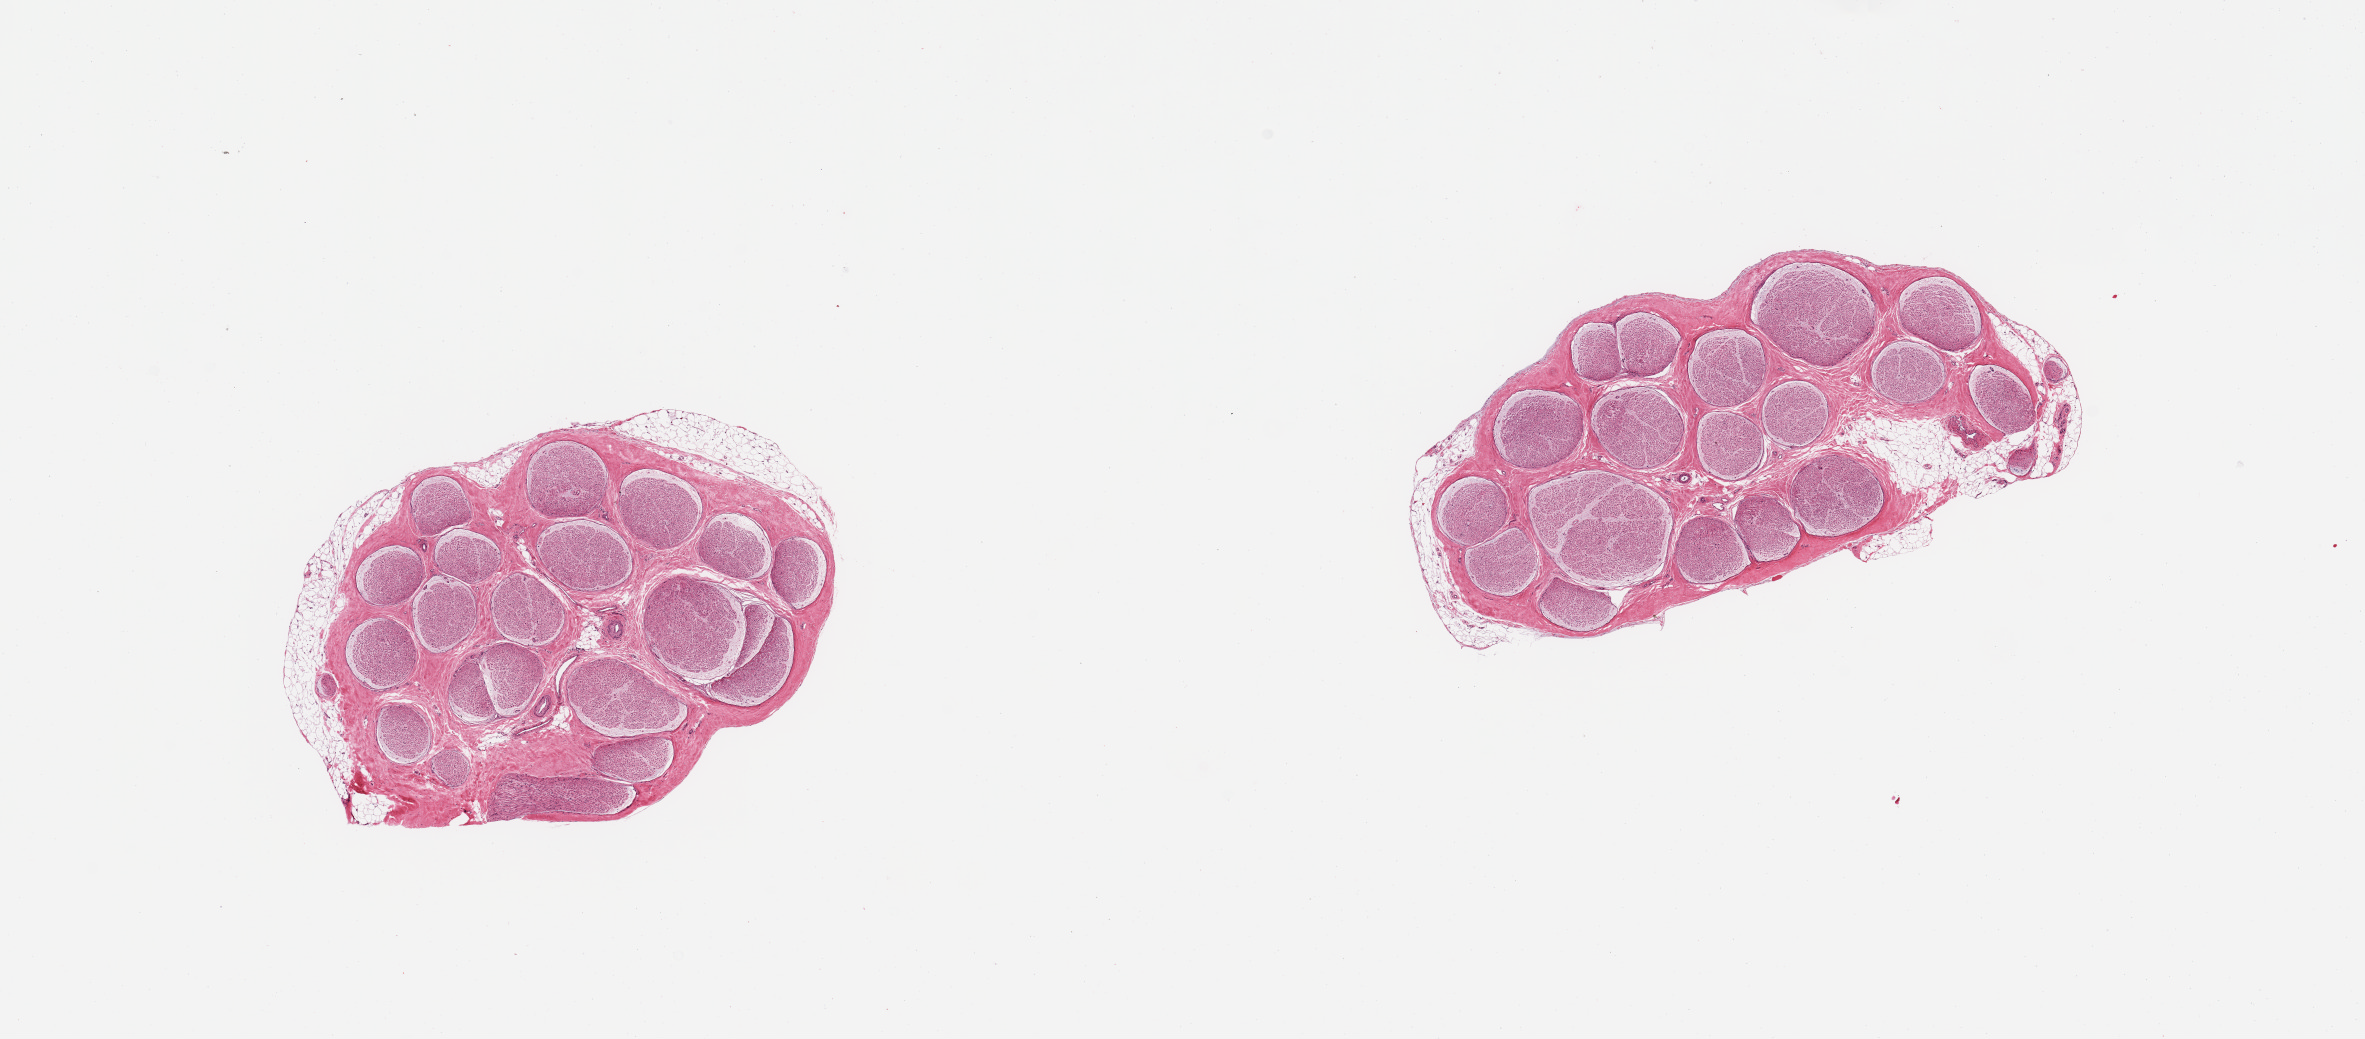
Whole-slide image, hematoxylin and eosin (H&E) stain — shown as a low-resolution overview of the whole scanned area (about 18.7 x 8.2 mm); PAXgene-fixed, paraffin-embedded tissue; section of tibial nerve (target tissue); tissue donor sample. Donor sex: male.
• pathologist's review note for this sample: 2 pieces, trace nubbins adherent fat